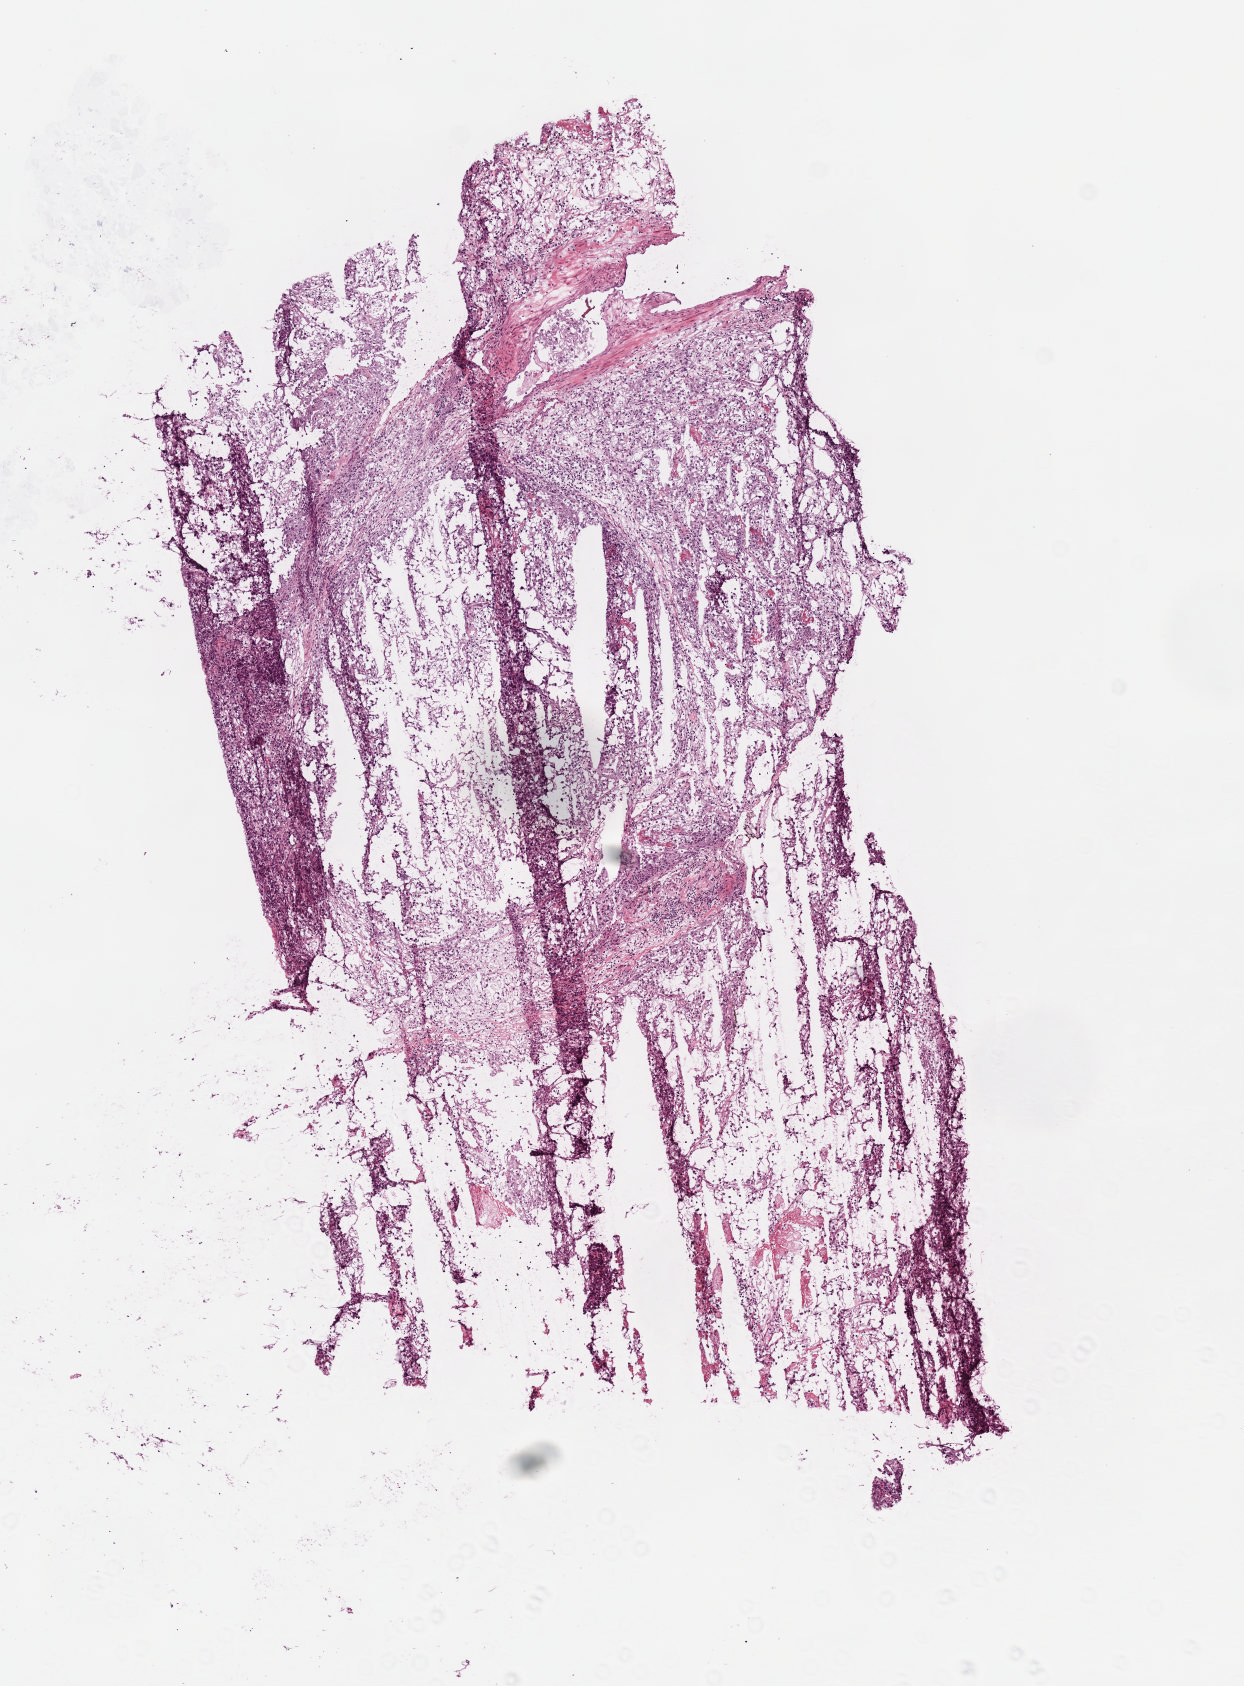
H&E-stained whole-slide image — a low-resolution overview of the entire scanned area, about 5.0 x 6.8 mm. Frozen section from the top of the tissue portion. Sample: primary tumour, kidney. Patient: male, age at initial diagnosis 79 years. Histologic grade: G3 (poorly differentiated). Composition of this section per pathologist review: tumour cells 95%, tumour nuclei 85%, normal cells 0%, stromal cells 5%, necrosis 0%.
TNM: T1a N0 M0. AJCC pathologic stage: I. Laterality: left. Pathologic diagnosis: Clear cell adenocarcinoma, NOS.